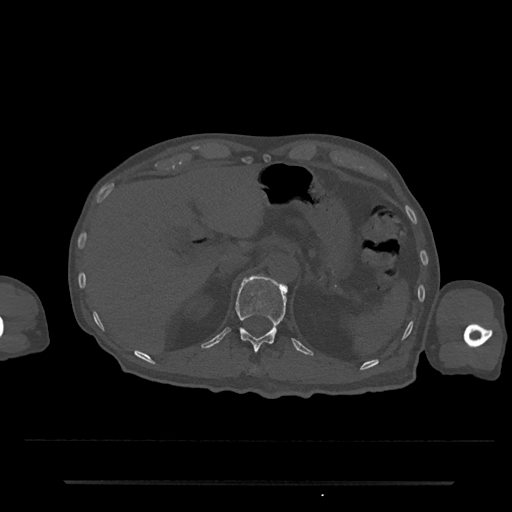
CT including the spine, one axial slice; reconstruction kernel Br40s/3; bone window (W 1800 / L 400 HU); 512 × 512 image matrix. Male patient, age 74 years. From the clinical record (not read from this slice): primary cancer: prostate.
Structures marked on this image (semi-automatic segmentation, software-assisted and operator-edited):
- T11 vertebra: bounding box <252,367,256,371> (left, top, right, bottom; pixels)
- T12 vertebra: <236,277,287,352>